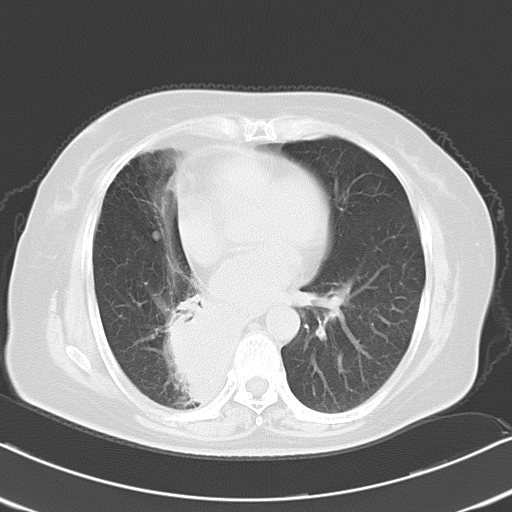
Chest CT, one axial slice; slice 9 of 21 in the series (ordered by position); reconstruction kernel B70f; 120 kVp; lung window (W 1500 / L -600 HU); 10 mm slice thickness; 512 × 512 image matrix. Patient: female, 61 years. Case-level facts recorded for this patient, not image findings: clinical TNM (as recorded): T1b N0 M1b.
Annotated regions visible in this slice (rectangle marked by the reading radiologist):
- lung tumour (recorded histology: squamous cell carcinoma): bounding box [x1, y1, x2, y2] px = [160, 288, 255, 432]